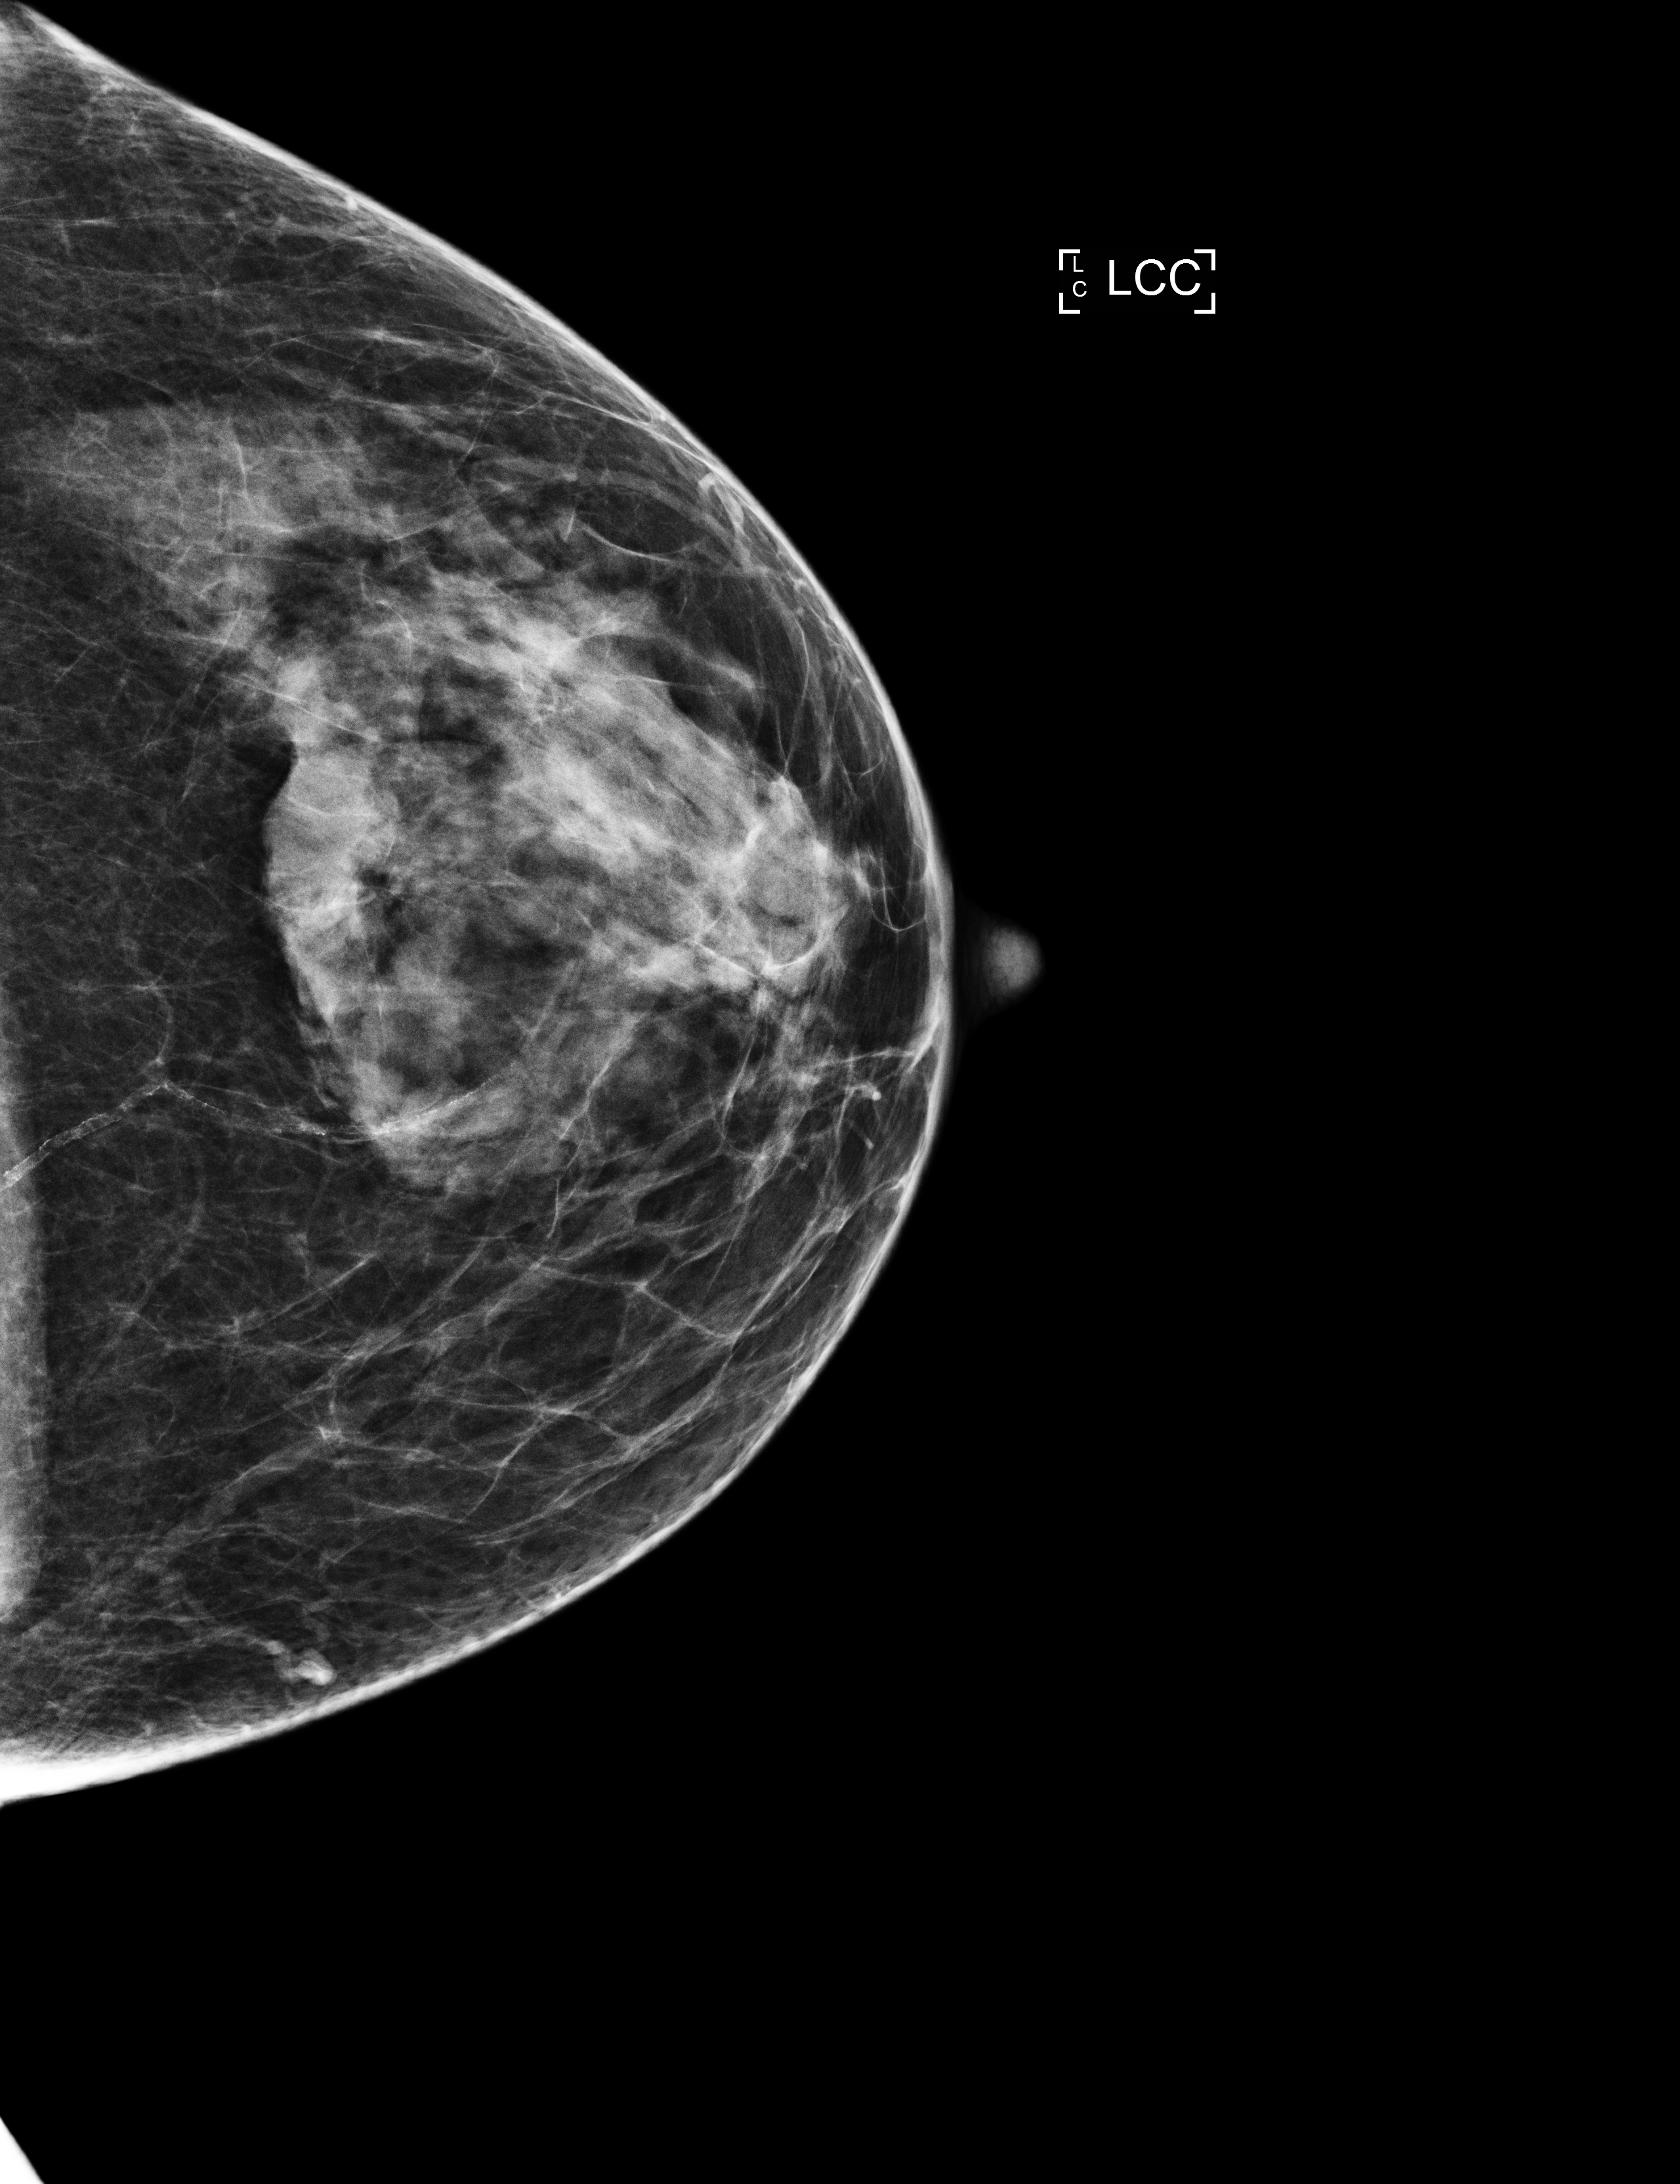
Full-field digital mammogram (FFDM), left breast, CC view, screening examination, compressed breast thickness 48 mm. Female patient, age 57 years.
- breast density at the screening exam (both breasts): heterogeneously dense (BI-RADS density category c)
- final BI-RADS category for the screening round (tomosynthesis exam, both breasts): category 1
- recall: no recall after this screen